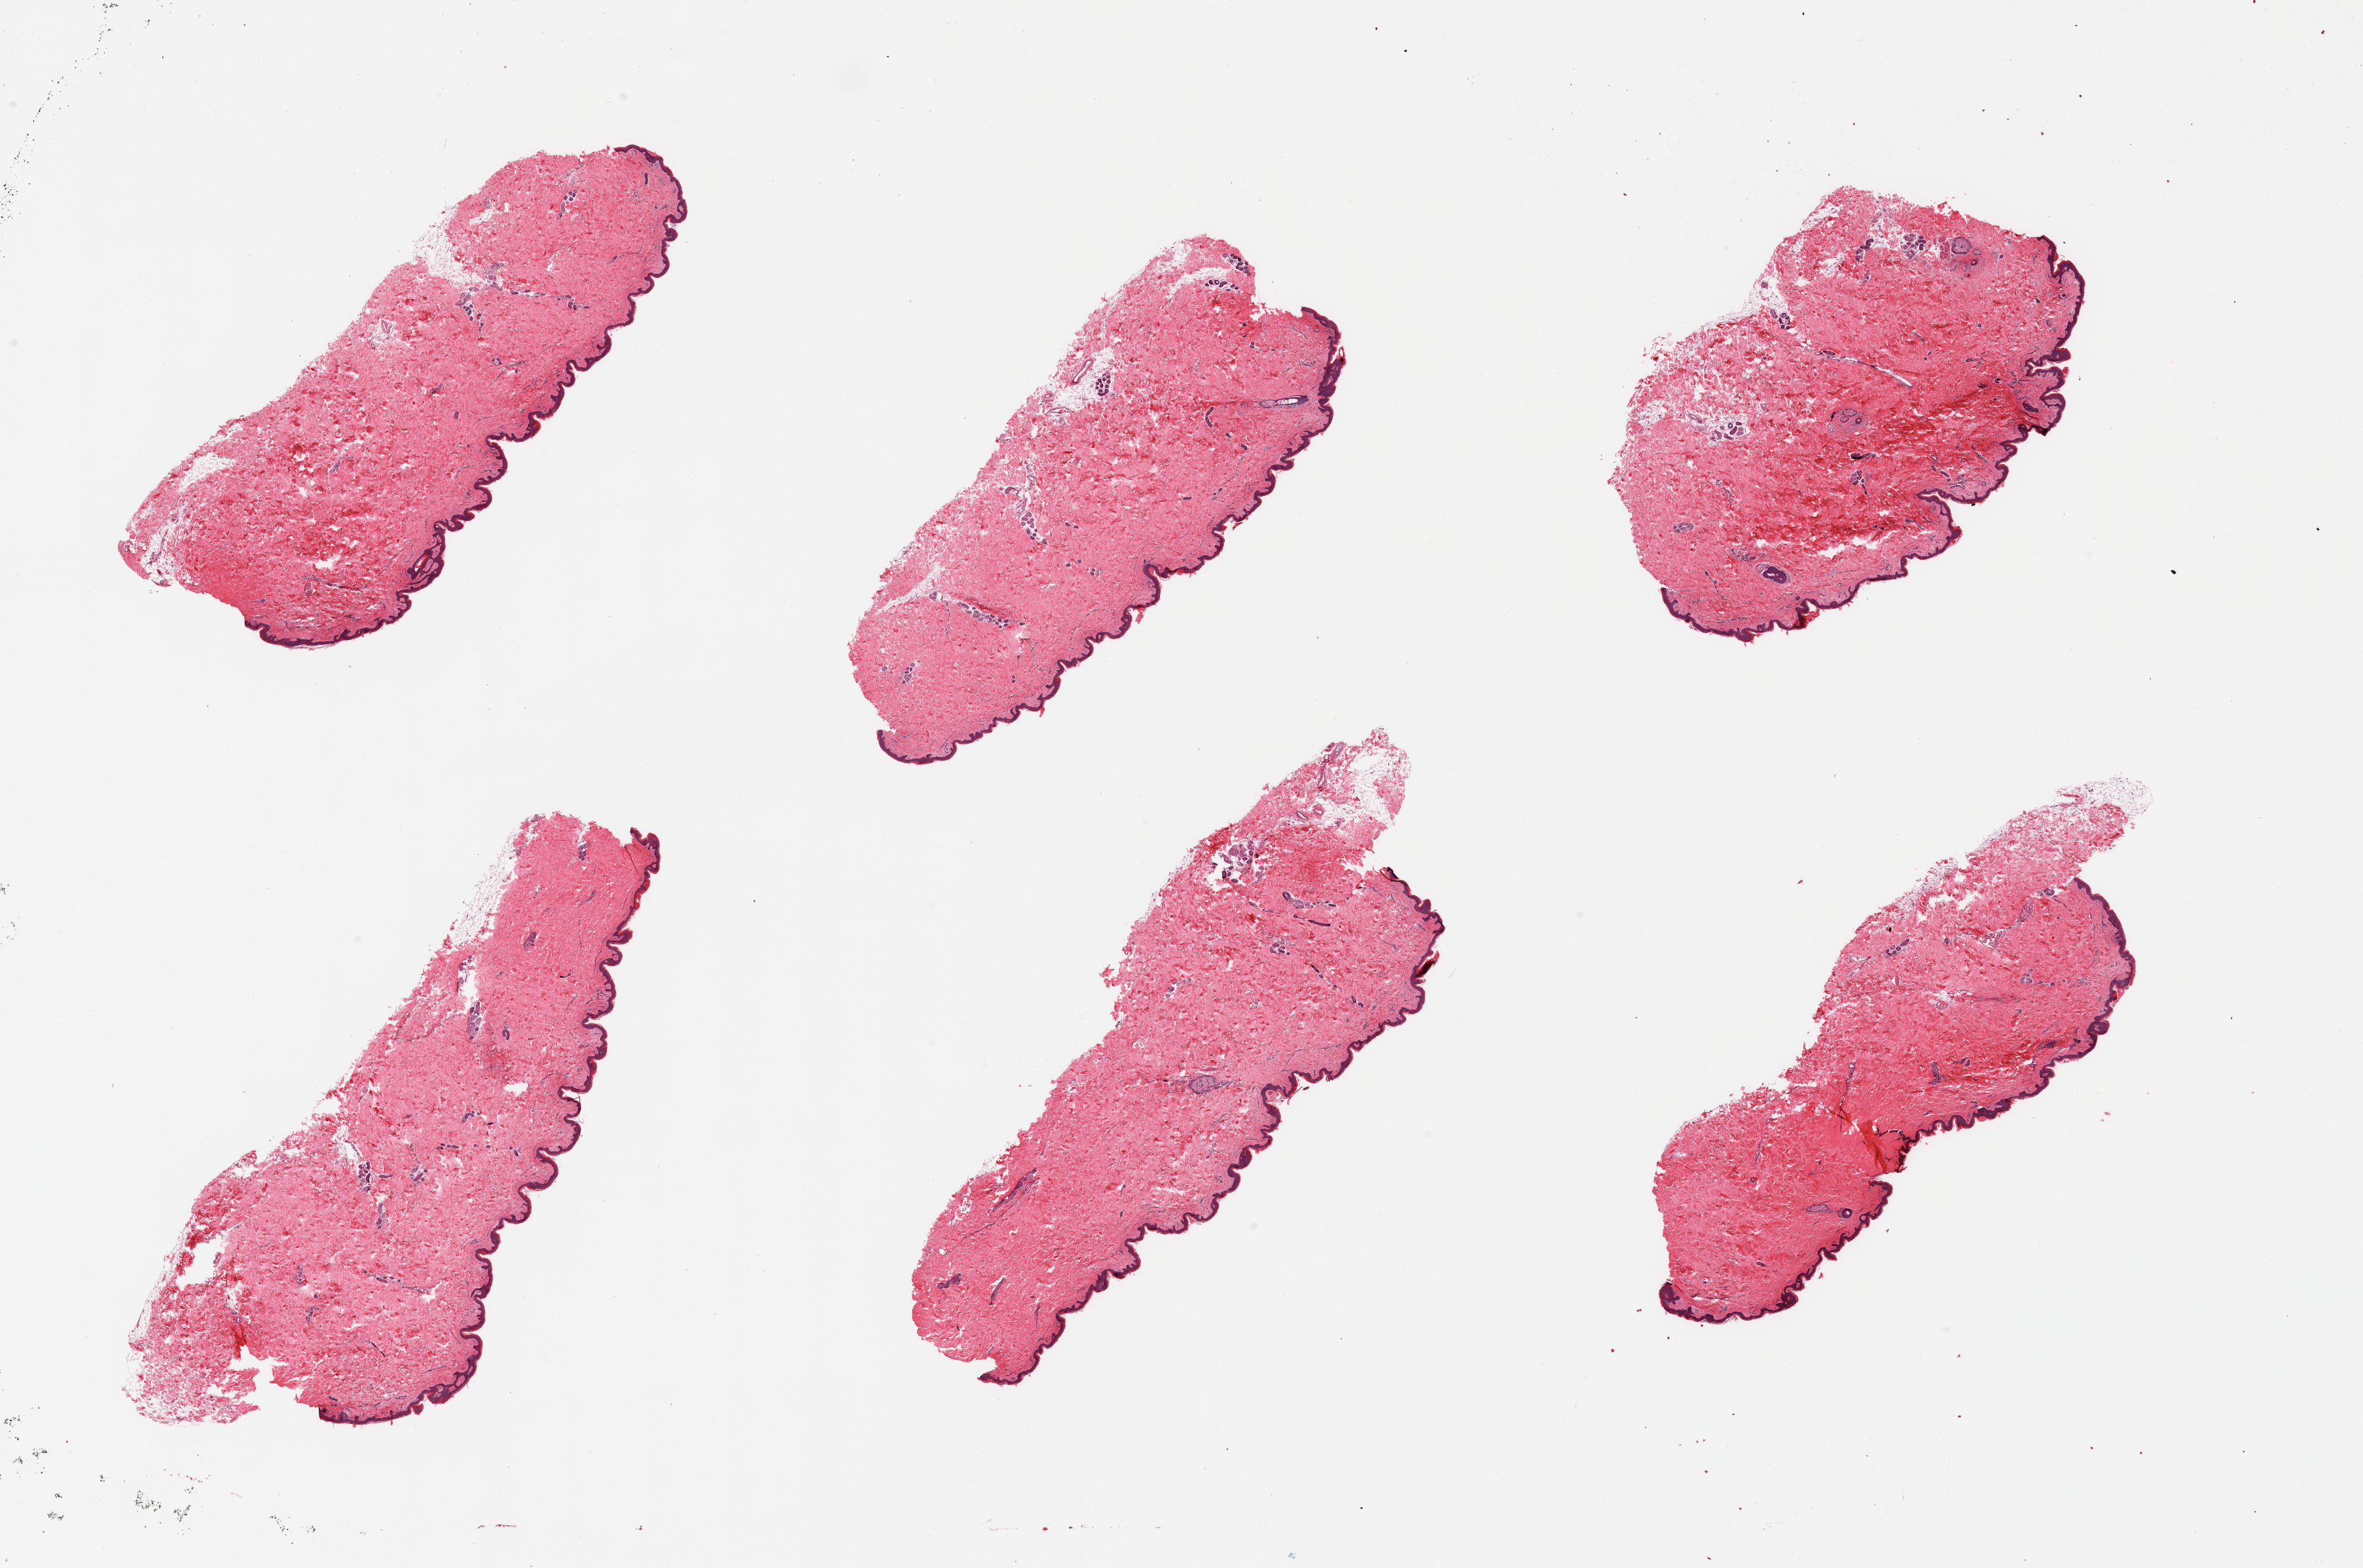
Hematoxylin and eosin (H&E) whole-slide image, brightfield, low-resolution overview of the scanned area, about 28.5 x 18.9 mm, PAXgene-fixed, paraffin-embedded tissue, target tissue: skin of suprapubic region, tissue donor sample. Female donor.
* pathologist's review note for this sample: 6 pieces; 5 to 10% internal fat